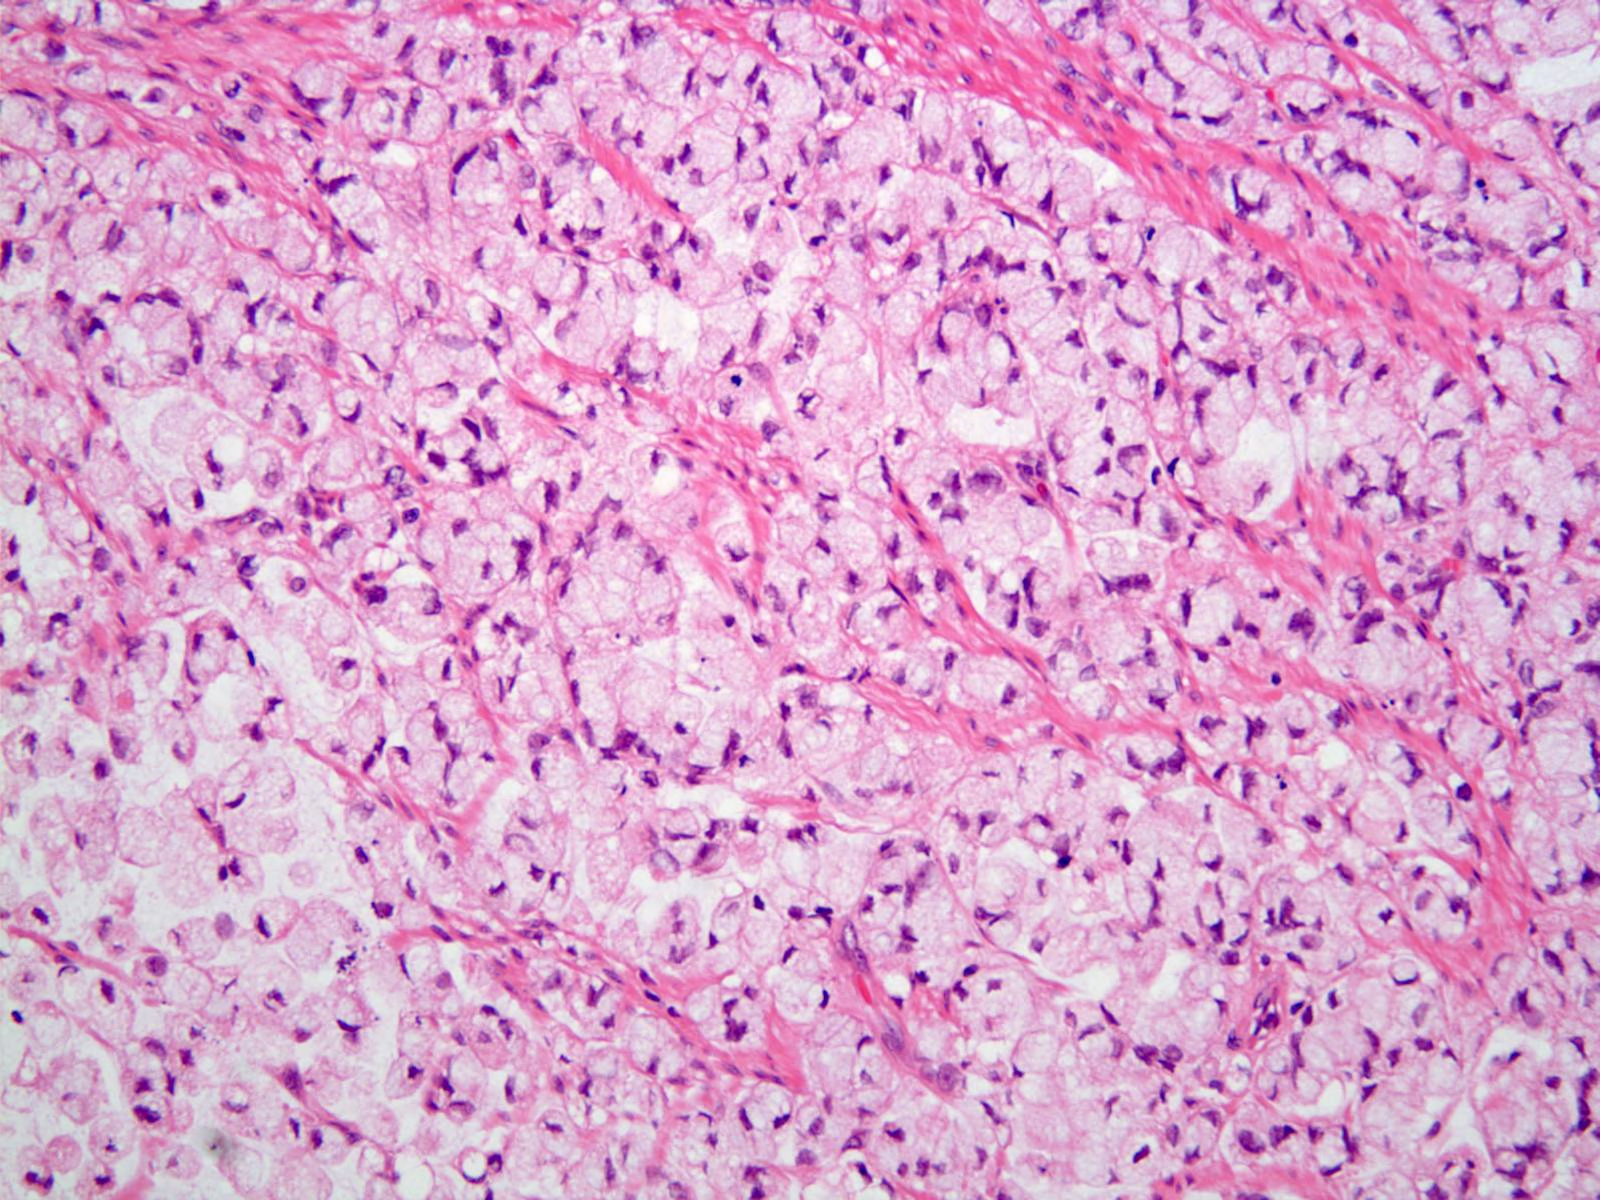
Hematoxylin and eosin (H&E) stained image of one small field of the section — covering about 0.8 x 0.6 mm, formalin-fixed paraffin-embedded (FFPE) diagnostic section, stomach, primary tumour sample. Patient: male, age at initial diagnosis 43 years. Histologic grade: G3 (poorly differentiated).
* AJCC pathologic stage: II (6th edition)
* histologic diagnosis: Adenocarcinoma, NOS